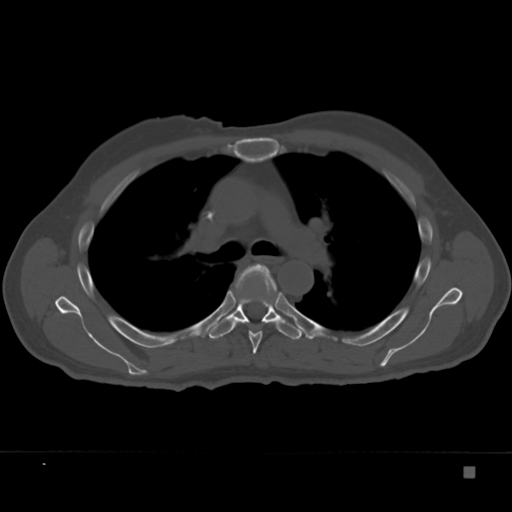
CT including the spine, one axial slice. Slice 248 of 332 in the series (ordered by position). Reconstruction kernel Br40s. Bone window (W 1800 / L 400 HU). 512 × 512 image matrix, field of view 389 × 389 mm. Patient: male, 72 years. Case-level facts recorded for this patient, not image findings: primary cancer: skeletal.
Structures marked on this image (semi-automatic segmentation, software-assisted and operator-edited):
- T5 vertebra: bounding box [x1, y1, x2, y2] px = [235, 264, 279, 354]
- T6 vertebra: [208, 282, 302, 340]